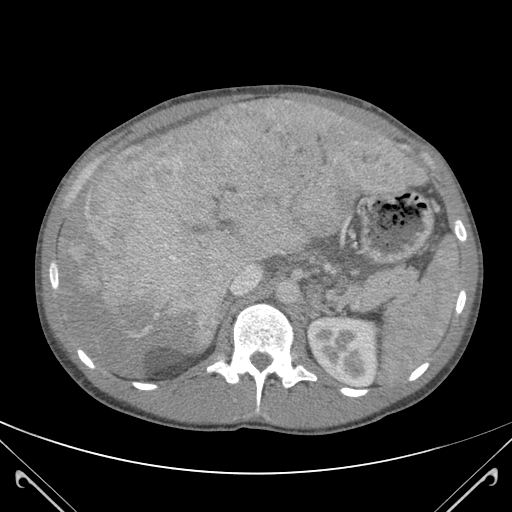
Contrast-enhanced abdominal CT (liver protocol), one axial slice. Position 75 of 118 along the scan axis. 120 kVp. Soft-tissue window (W 400 / L 40 HU). 512 × 512 image matrix, field of view 380 × 380 mm. Case-level facts recorded for this patient, not image findings: diagnosis: hepatocellular carcinoma (patient treated with transarterial chemoembolisation; whether this scan precedes or follows treatment is not stated here); TNM stage (as recorded): Stage-IIIB; Child-Pugh class: A.
Outlined on this slice (semi-automatically segmented with operator editing):
- abdominal aorta: bounding box [x1, y1, x2, y2] px = [276, 280, 298, 305]
- liver parenchyma outside the tumour (the mass and vessels are separate outlines, so this box may not span the whole liver): [58, 101, 409, 378]
- mass: [63, 101, 427, 354]
- liver vessels: [230, 101, 386, 295]